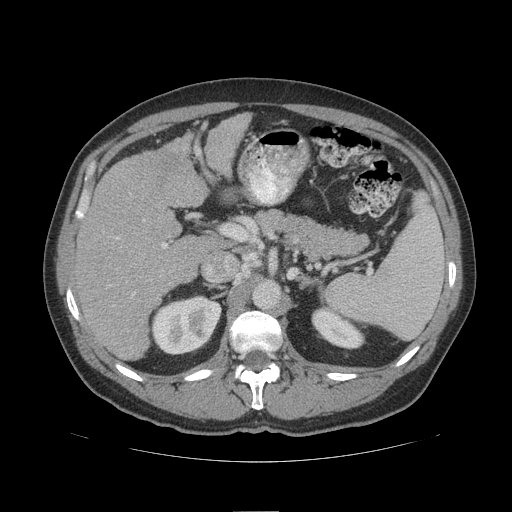
Contrast-enhanced abdominal CT (liver protocol), one axial slice. Position 61 of 109 along the scan axis. Reconstruction kernel STANDARD. 140 kVp. Soft-tissue window (W 400 / L 40 HU). 2.5 mm slice thickness. 512 × 512 image matrix. Case-level facts recorded for this patient, not image findings: diagnosis: hepatocellular carcinoma (patient treated with transarterial chemoembolisation; whether this scan precedes or follows treatment is not stated here); TNM stage (as recorded): Stage-IIIB; Child-Pugh class: A; tumour differentiation: poorly differentiated; tumour nodularity: multinodular.
Outlined on this slice (semi-automatic segmentation, software-assisted and operator-edited):
- liver parenchyma outside the tumour (the mass and vessels are separate outlines, so this box may not span the whole liver): box from (x=74, y=112) to (x=250, y=360) px
- liver vessels: (x=162, y=243)–(x=167, y=248)